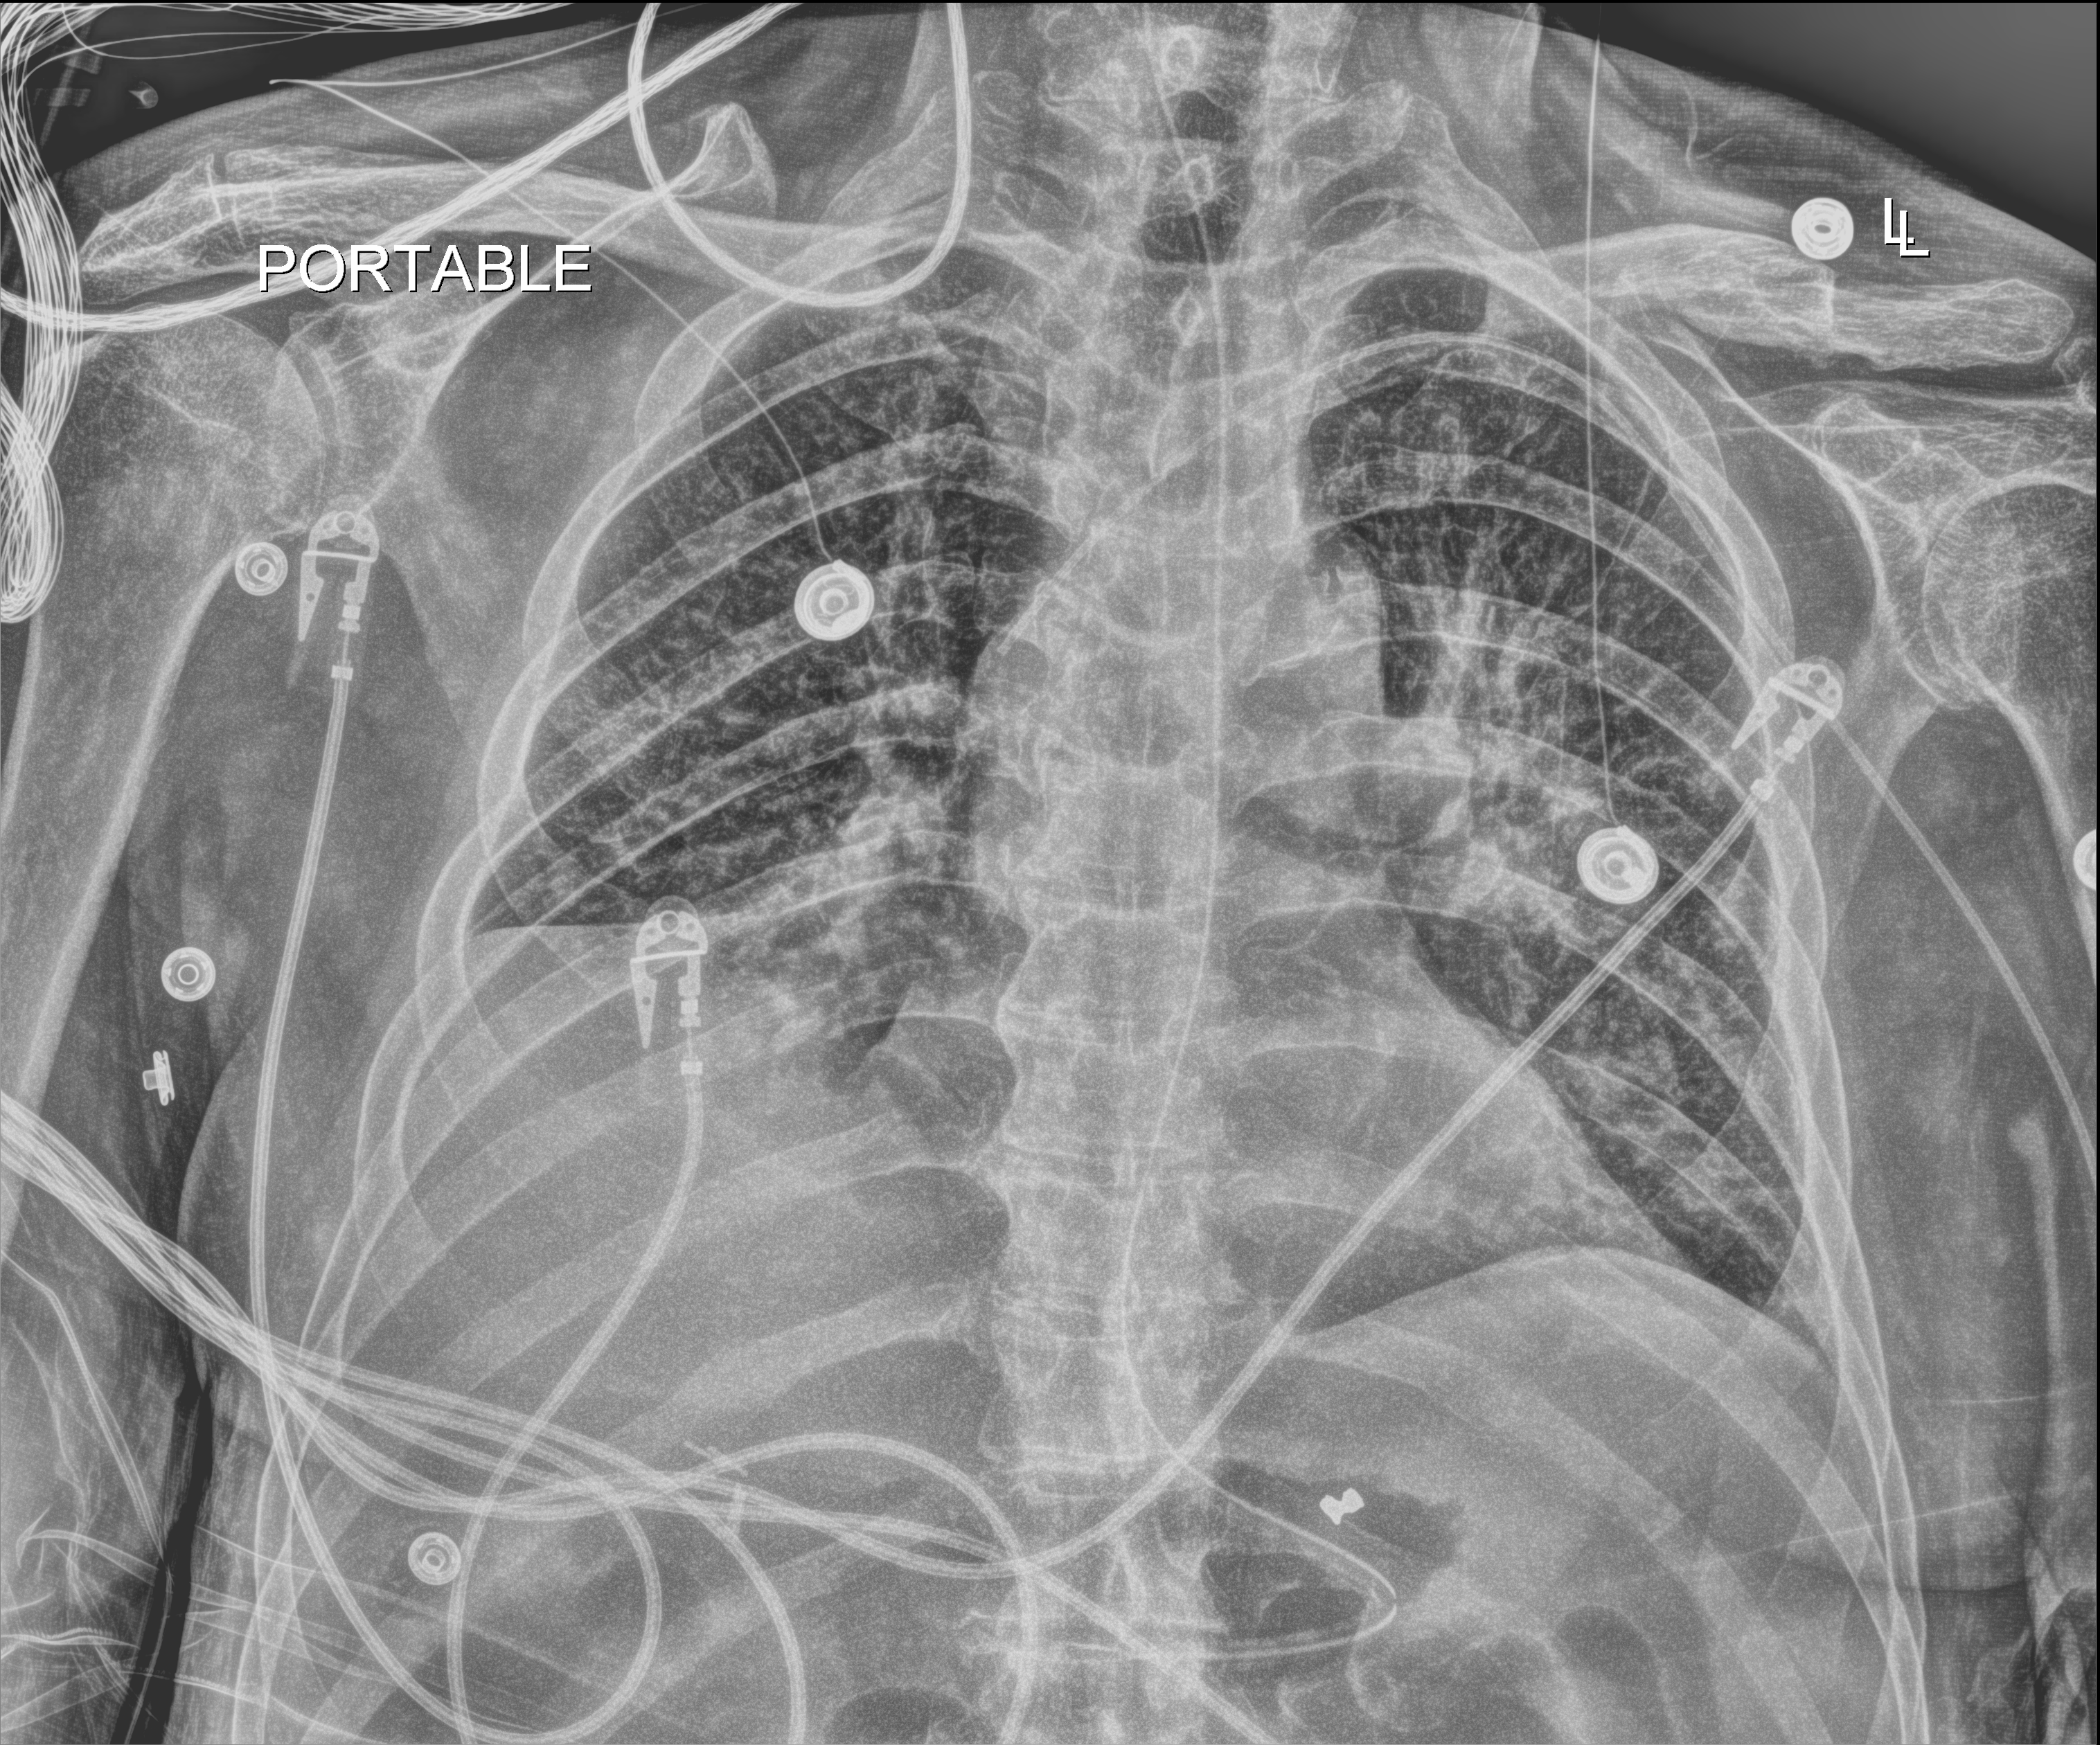
Chest X-ray (portable); anteroposterior (AP) projection. Male patient hospitalised with COVID-19, age 60–74 years.
Admission-level facts for this patient (not findings on this image; timing relative to this image not recorded): length of hospital stay: 5 days; admitted to intensive care during this hospital stay: no; mechanically ventilated during this hospital stay: no.